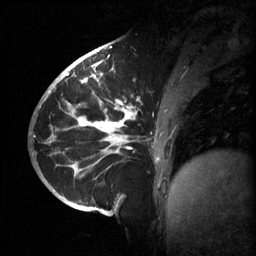
Breast MRI (dynamic contrast-enhanced), one sagittal slice. Slice 22 of 60 in the series (ordered by position). 3 images stored at this slice position (order not interpretable as contrast timing). 1.5 T. TE 4.2 ms, TR 11 ms. 256 × 256 image matrix, field of view 220 × 220 mm. Patient: female, 51 years.
Annotated regions visible in this slice (semi-automatic segmentation, software-assisted and operator-edited):
- analysis volume of interest (the breast-tissue region the enhancement analysis was run in; not a lesion): bounding box (x1, y1, x2, y2) in pixels: (63, 80, 187, 201)
- tumour enhancement mask (voxels above the 70 % enhancement threshold inside the analysis volume of interest): (67, 80, 160, 169)